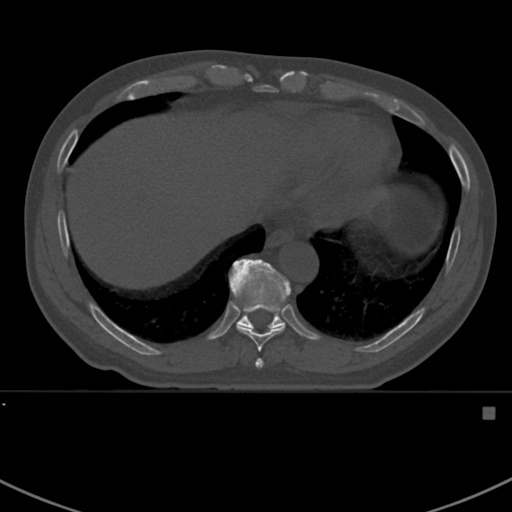
CT including the spine, one axial slice; position 377 of 412 along the scan axis; 120 kVp; bone window (W 1800 / L 400 HU); 1.5 mm slice thickness; 512 × 512 image matrix, field of view 358 × 358 mm. Male patient, age 59 years. Case-level facts recorded for this patient, not image findings: primary cancer: prostate.
Outlined on this slice (semi-automatically segmented with operator editing):
- T10 vertebra: box from (x=230, y=259) to (x=291, y=329) px
- T8 vertebra: (x=255, y=359)–(x=264, y=368)
- T9 vertebra: (x=238, y=327)–(x=284, y=352)